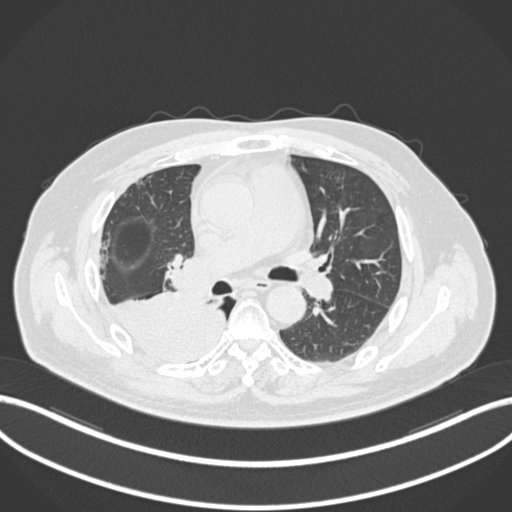
Chest CT, one axial slice; slice 110 of 218 in the series (ordered by position); reconstruction kernel B30f; lung window (W 1500 / L -600 HU); 512 × 512 image matrix, field of view 400 × 400 mm. Male patient, age 68 years. Case-level facts recorded for this patient, not image findings: clinical TNM (as recorded): T2a N0 M0.
Annotated regions visible in this slice (bounding box drawn by a radiologist):
- lung tumour (recorded histology: adenocarcinoma): bounding box <106,289,226,371> (left, top, right, bottom; pixels)